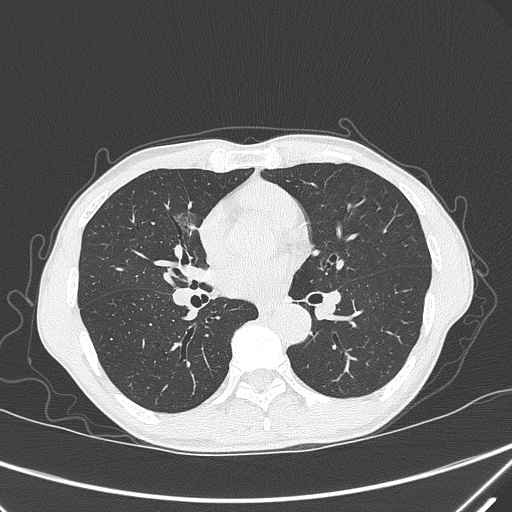
Chest CT, one axial slice; position 169 of 339 along the scan axis; 120 kVp; lung window (W 1500 / L -600 HU); 1 mm slice thickness; 512 × 512 image matrix. Male patient, age 67 years. Case-level facts recorded for this patient, not image findings: clinical TNM (as recorded): T1c N0 M0; histopathological grade: G1-2.
Outlined on this slice (bounding box drawn by a radiologist):
- lung tumour (recorded histology: adenocarcinoma): box from (x=164, y=202) to (x=198, y=241) px